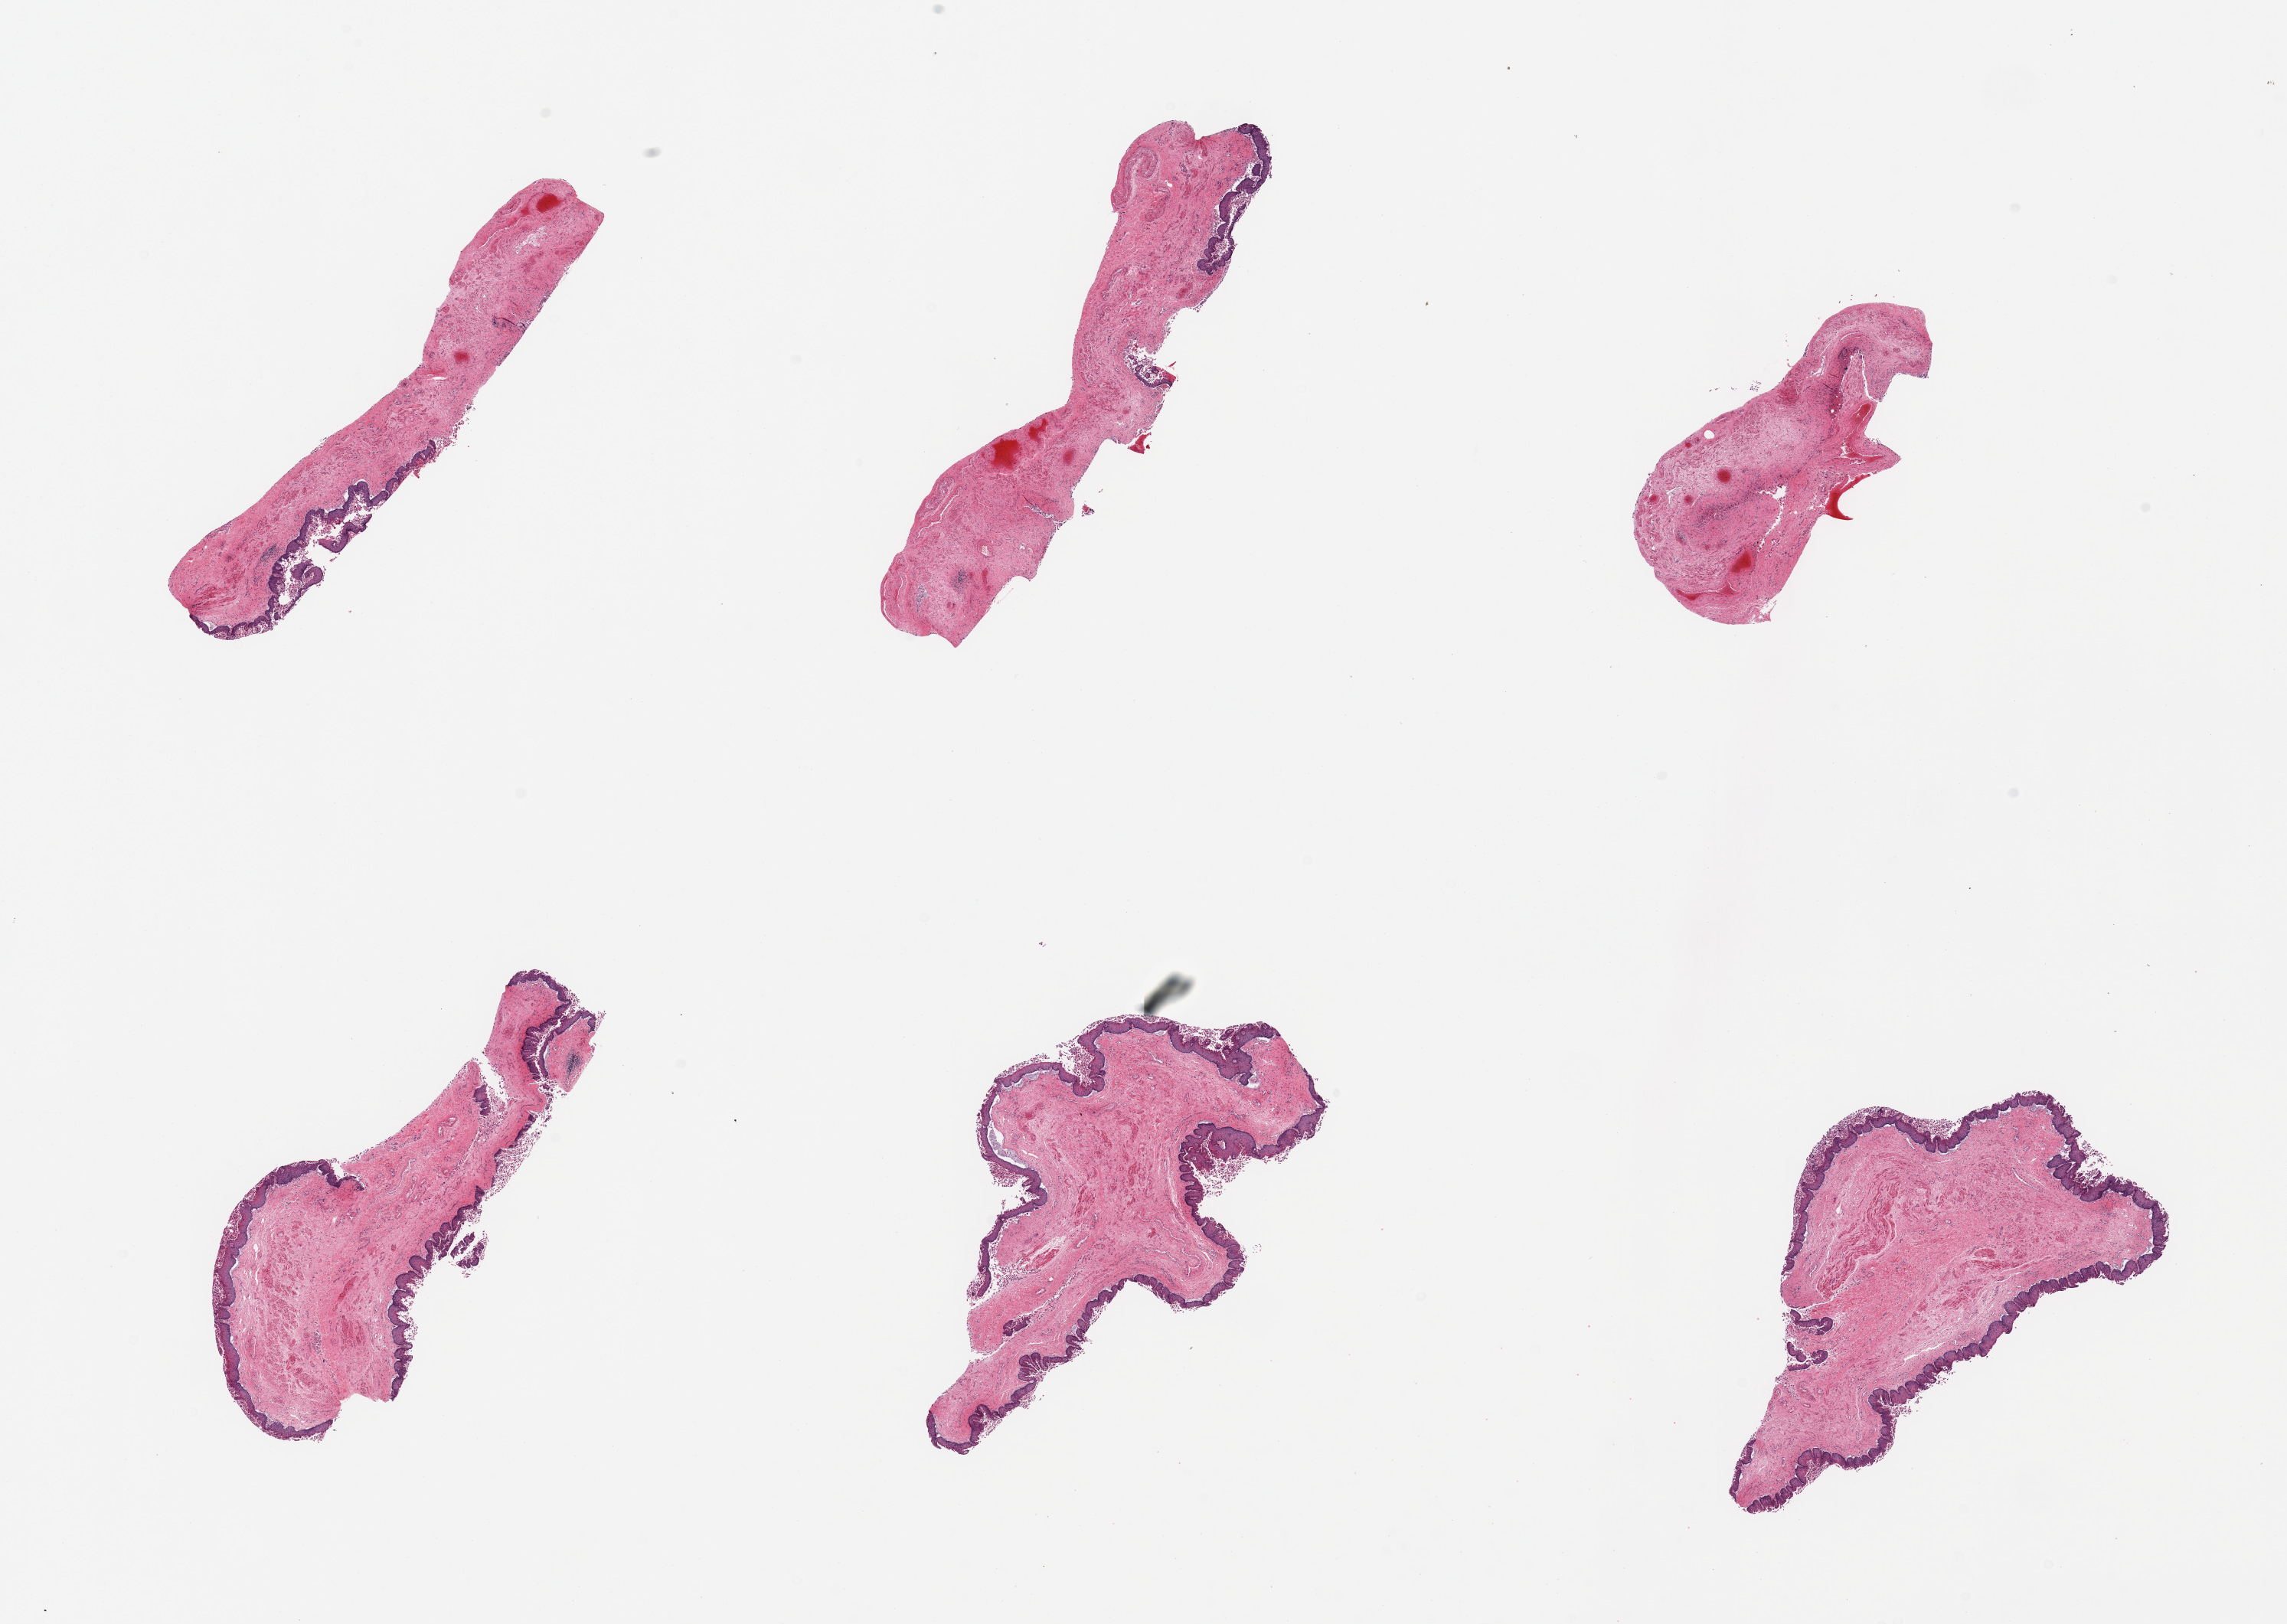
Digitized haematoxylin and eosin-stained section, brightfield, whole scanned area (about 23.6 x 16.8 mm, acquisition: 20x scan) shown as a low-resolution overview, PAXgene-fixed paraffin-embedded (PFPE) section, section of esophageal mucous membrane (target tissue), donor tissue sample. Donor sex: female.
Reviewer comment on this tissue sample: 6 pieces; moderately sloughed epithelium with several large bare spots.